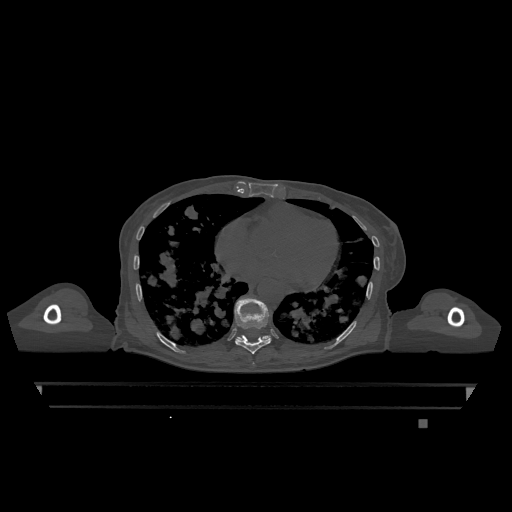
CT including the spine, one axial slice; position 681 of 1317 along the scan axis; bone window (W 1800 / L 400 HU); 0.5 mm slice thickness; 512 × 512 image matrix, field of view 500 × 500 mm. Patient: female, 74 years. Case-level facts recorded for this patient, not image findings: primary cancer: lung.
Outlined on this slice (semi-automatically segmented with operator editing):
- T10 vertebra: bounding box (x1, y1, x2, y2) in pixels: (237, 335, 270, 340)
- T9 vertebra: (235, 297, 271, 354)